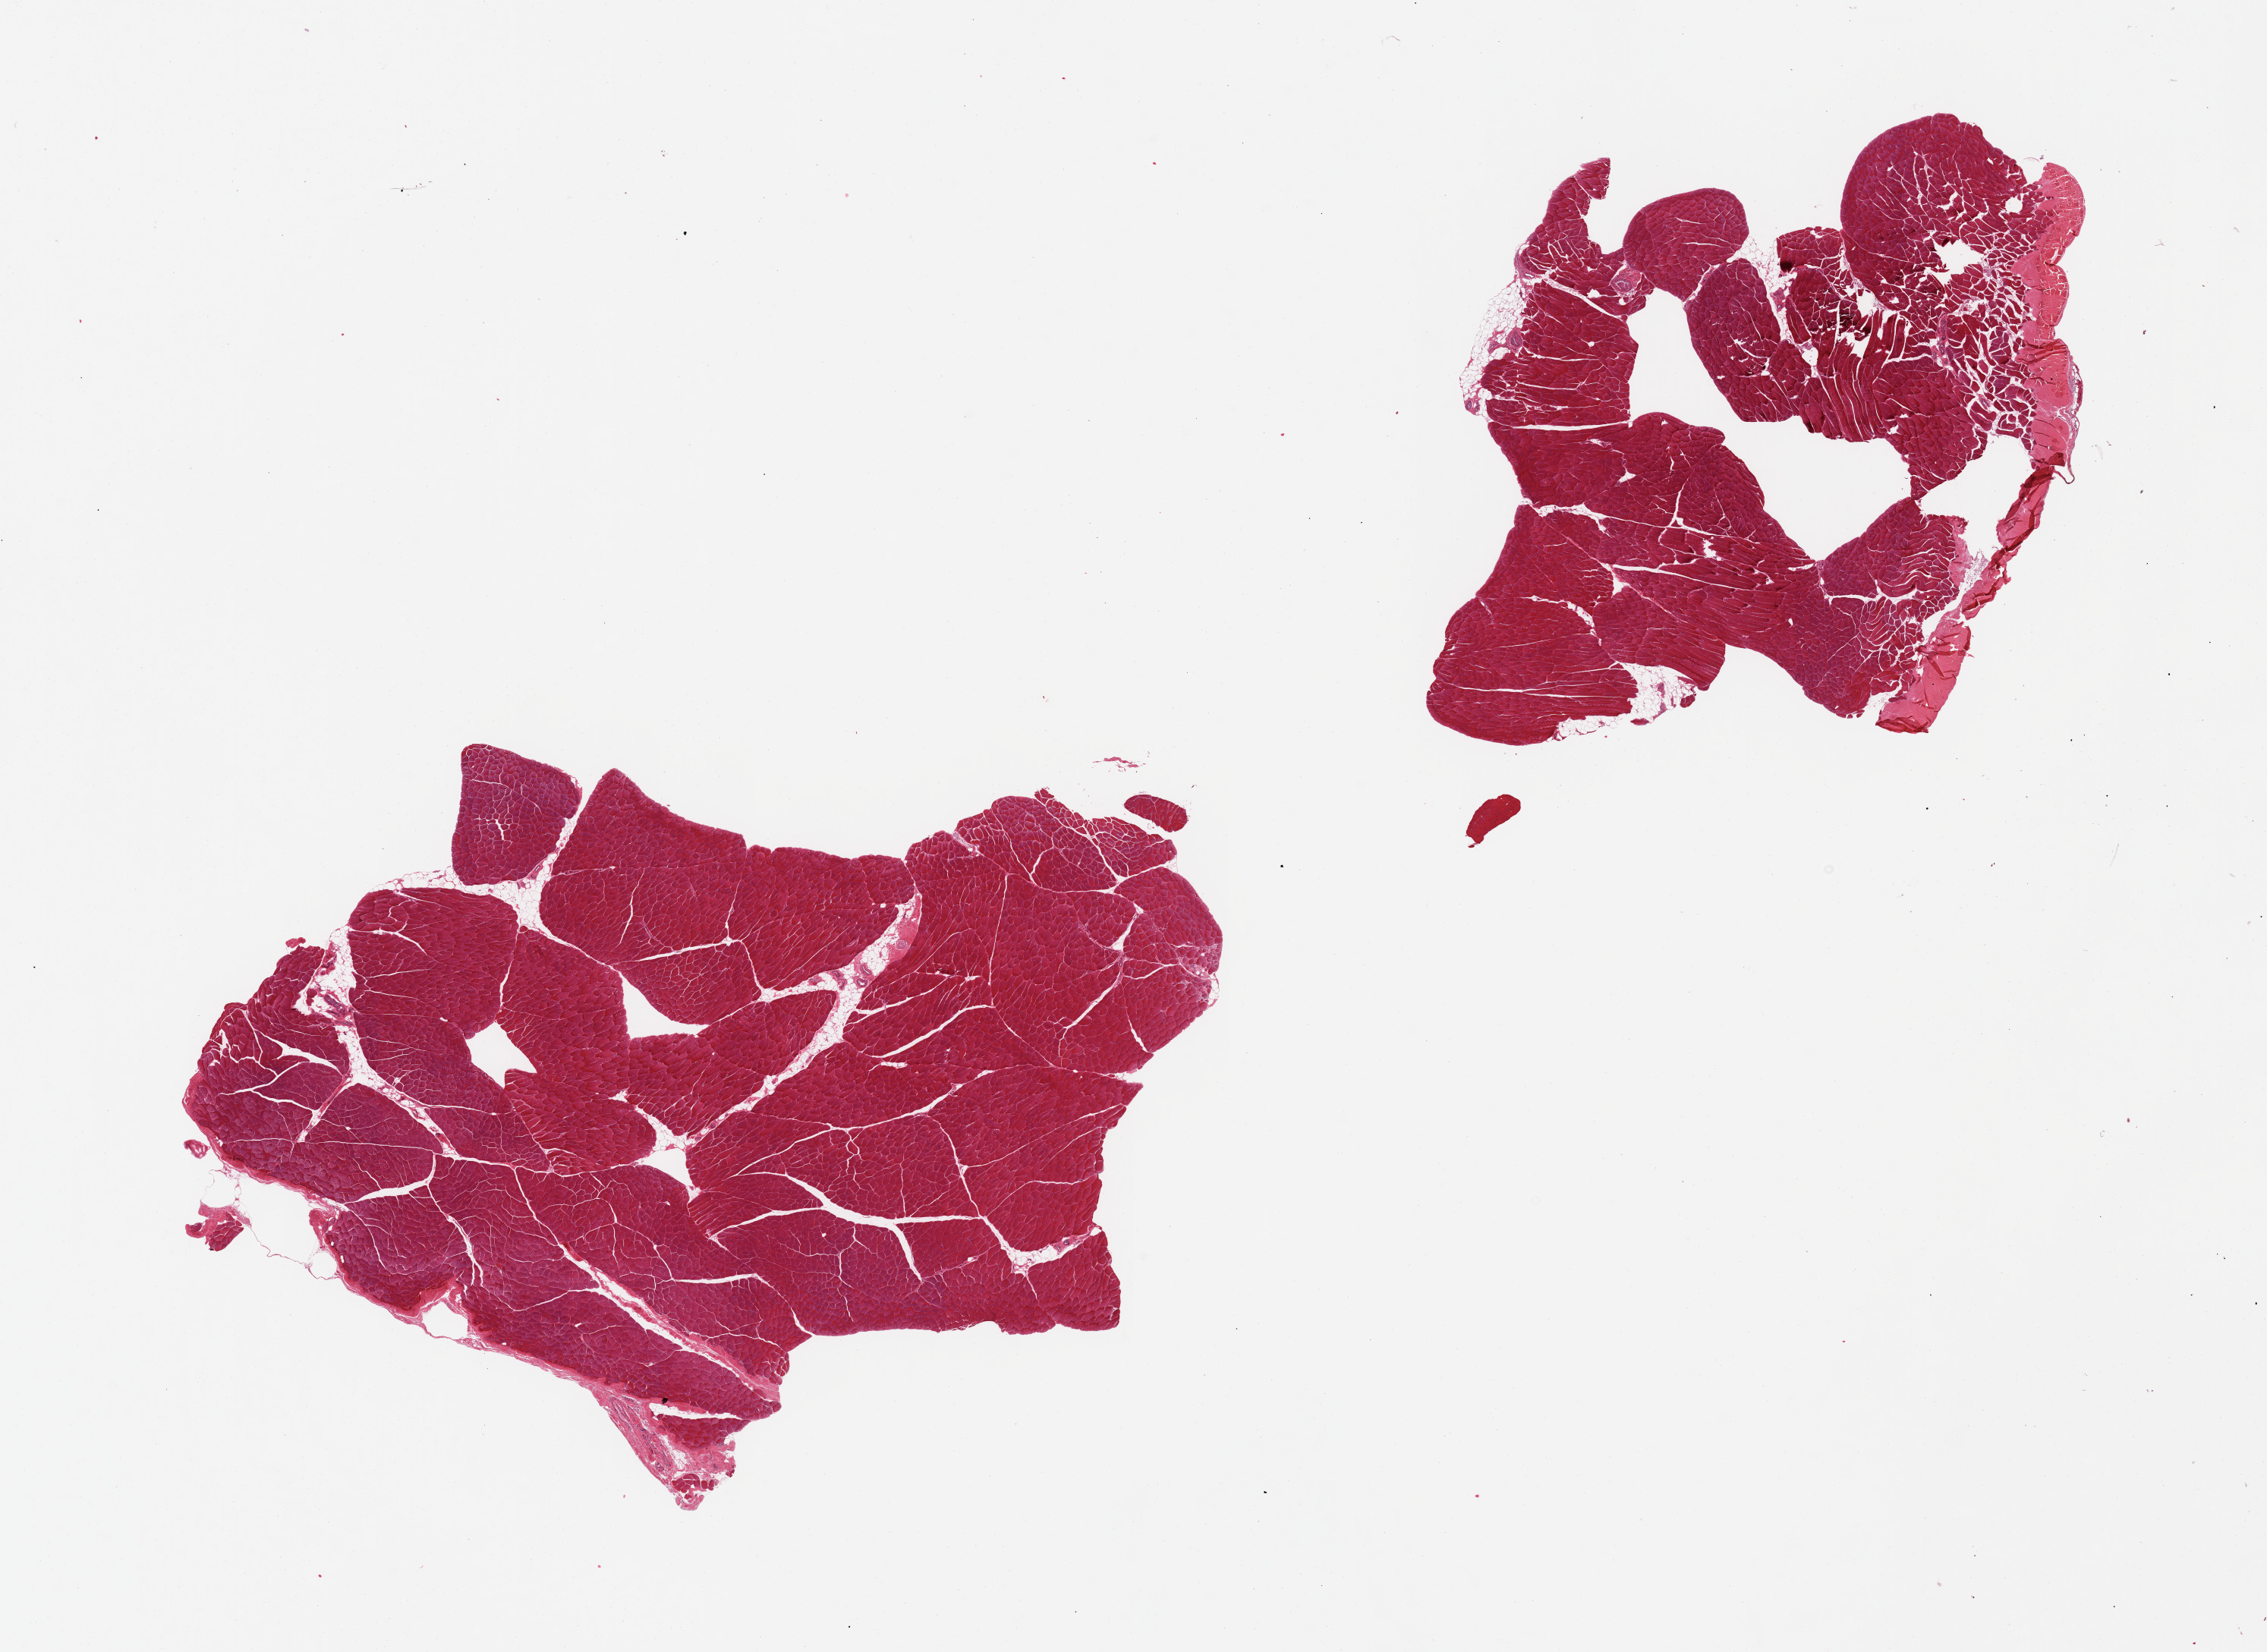
Digitized hematoxylin and eosin (H&E)-stained section, brightfield — low-resolution overview of the scanned area, about 23.6 x 17.2 mm, PAXgene-fixed, paraffin-embedded tissue, target tissue: skeletal muscle, donor tissue sample. Male donor.
Review note (as recorded): 2 pieces, skeletal muscle with <10% attached/internal fat, attached portion of tendon.